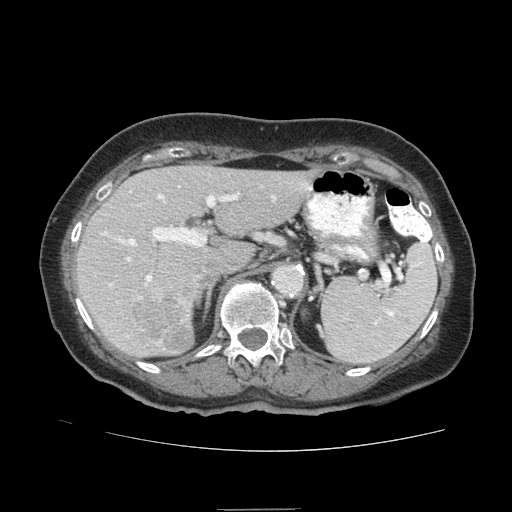
Contrast-enhanced abdominal CT (liver protocol), one axial slice. Slice 49 of 95 in the series (ordered by position). 140 kVp. Soft-tissue window (W 400 / L 40 HU). 2.5 mm slice thickness. 512 × 512 image matrix. From the clinical record (not read from this slice): diagnosis: hepatocellular carcinoma (patient treated with transarterial chemoembolisation; whether this scan precedes or follows treatment is not stated here); TNM stage (as recorded): Stage-IVA; Child-Pugh class: B; tumour differentiation: moderately differentiated.
Outlined on this slice (semi-automatic segmentation, software-assisted and operator-edited):
- liver parenchyma outside the tumour (the mass and vessels are separate outlines, so this box may not span the whole liver): box from (x=76, y=165) to (x=317, y=356) px
- mass: (x=134, y=282)–(x=197, y=353)
- liver vessels: (x=104, y=184)–(x=311, y=286)